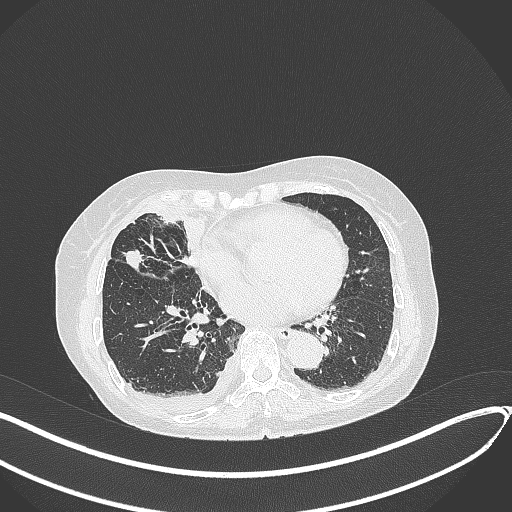
Chest CT, one axial slice; 120 kVp; lung window (W 1500 / L -600 HU); 1 mm slice thickness; 512 × 512 image matrix, field of view 400 × 400 mm. Patient: female, 75 years. From the clinical record (not read from this slice): clinical TNM (as recorded): T2a N3 M0.
Structures marked on this image (bounding box drawn by a radiologist):
- lung tumour (recorded histology: adenocarcinoma): box from (x=123, y=245) to (x=147, y=272) px